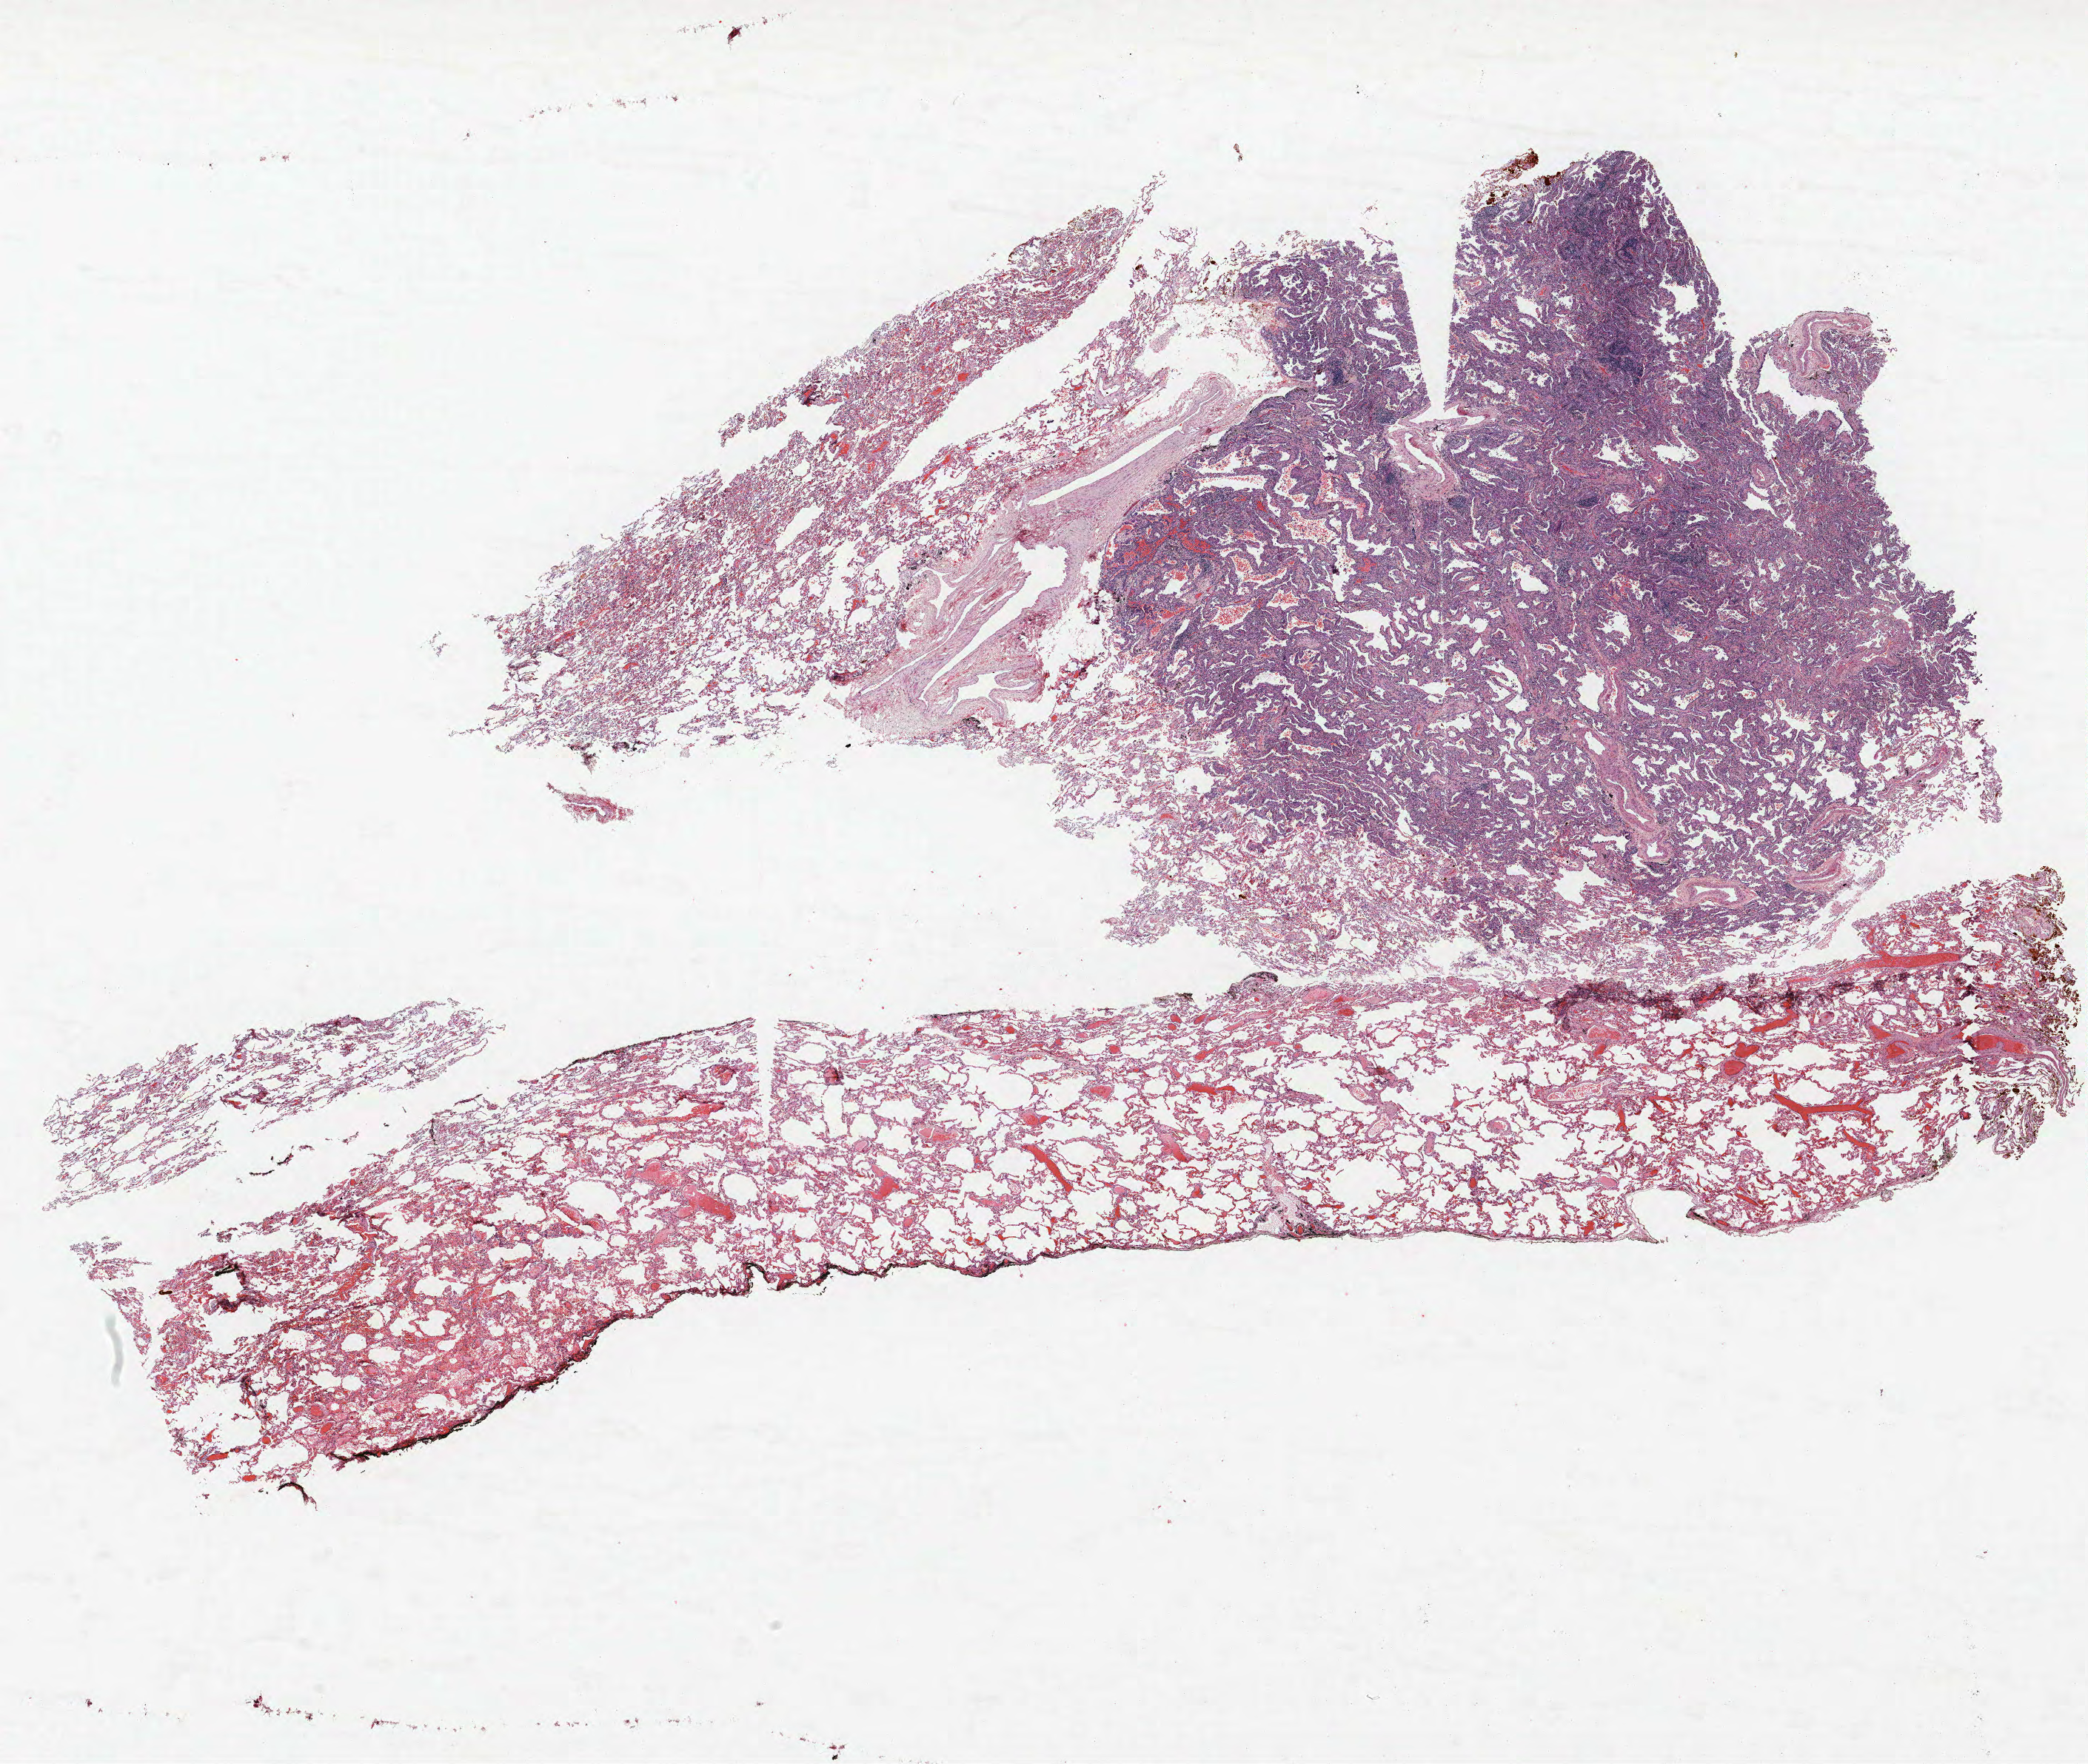
Whole-slide histology image, Hematoxylin and eosin (H&E) stained, whole scanned area (about 22.6 x 19.1 mm) shown as a low-resolution overview; FFPE section; lung. Male patient, aged 62 at enrolment. Former smoker at enrolment. Grade: well differentiated (G1).
- primary tumour location (clinical record): right lower lobe
- stage (AJCC 6th edition): IA
- participant's lung-cancer diagnosis: Bronchiolo-alveolar carcinoma, non-mucinous (ICD-O-3 8252/3)
- tumour size (pathology): 14 mm
- ICD-O-3 topography: lower lobe of lung (C34.3)